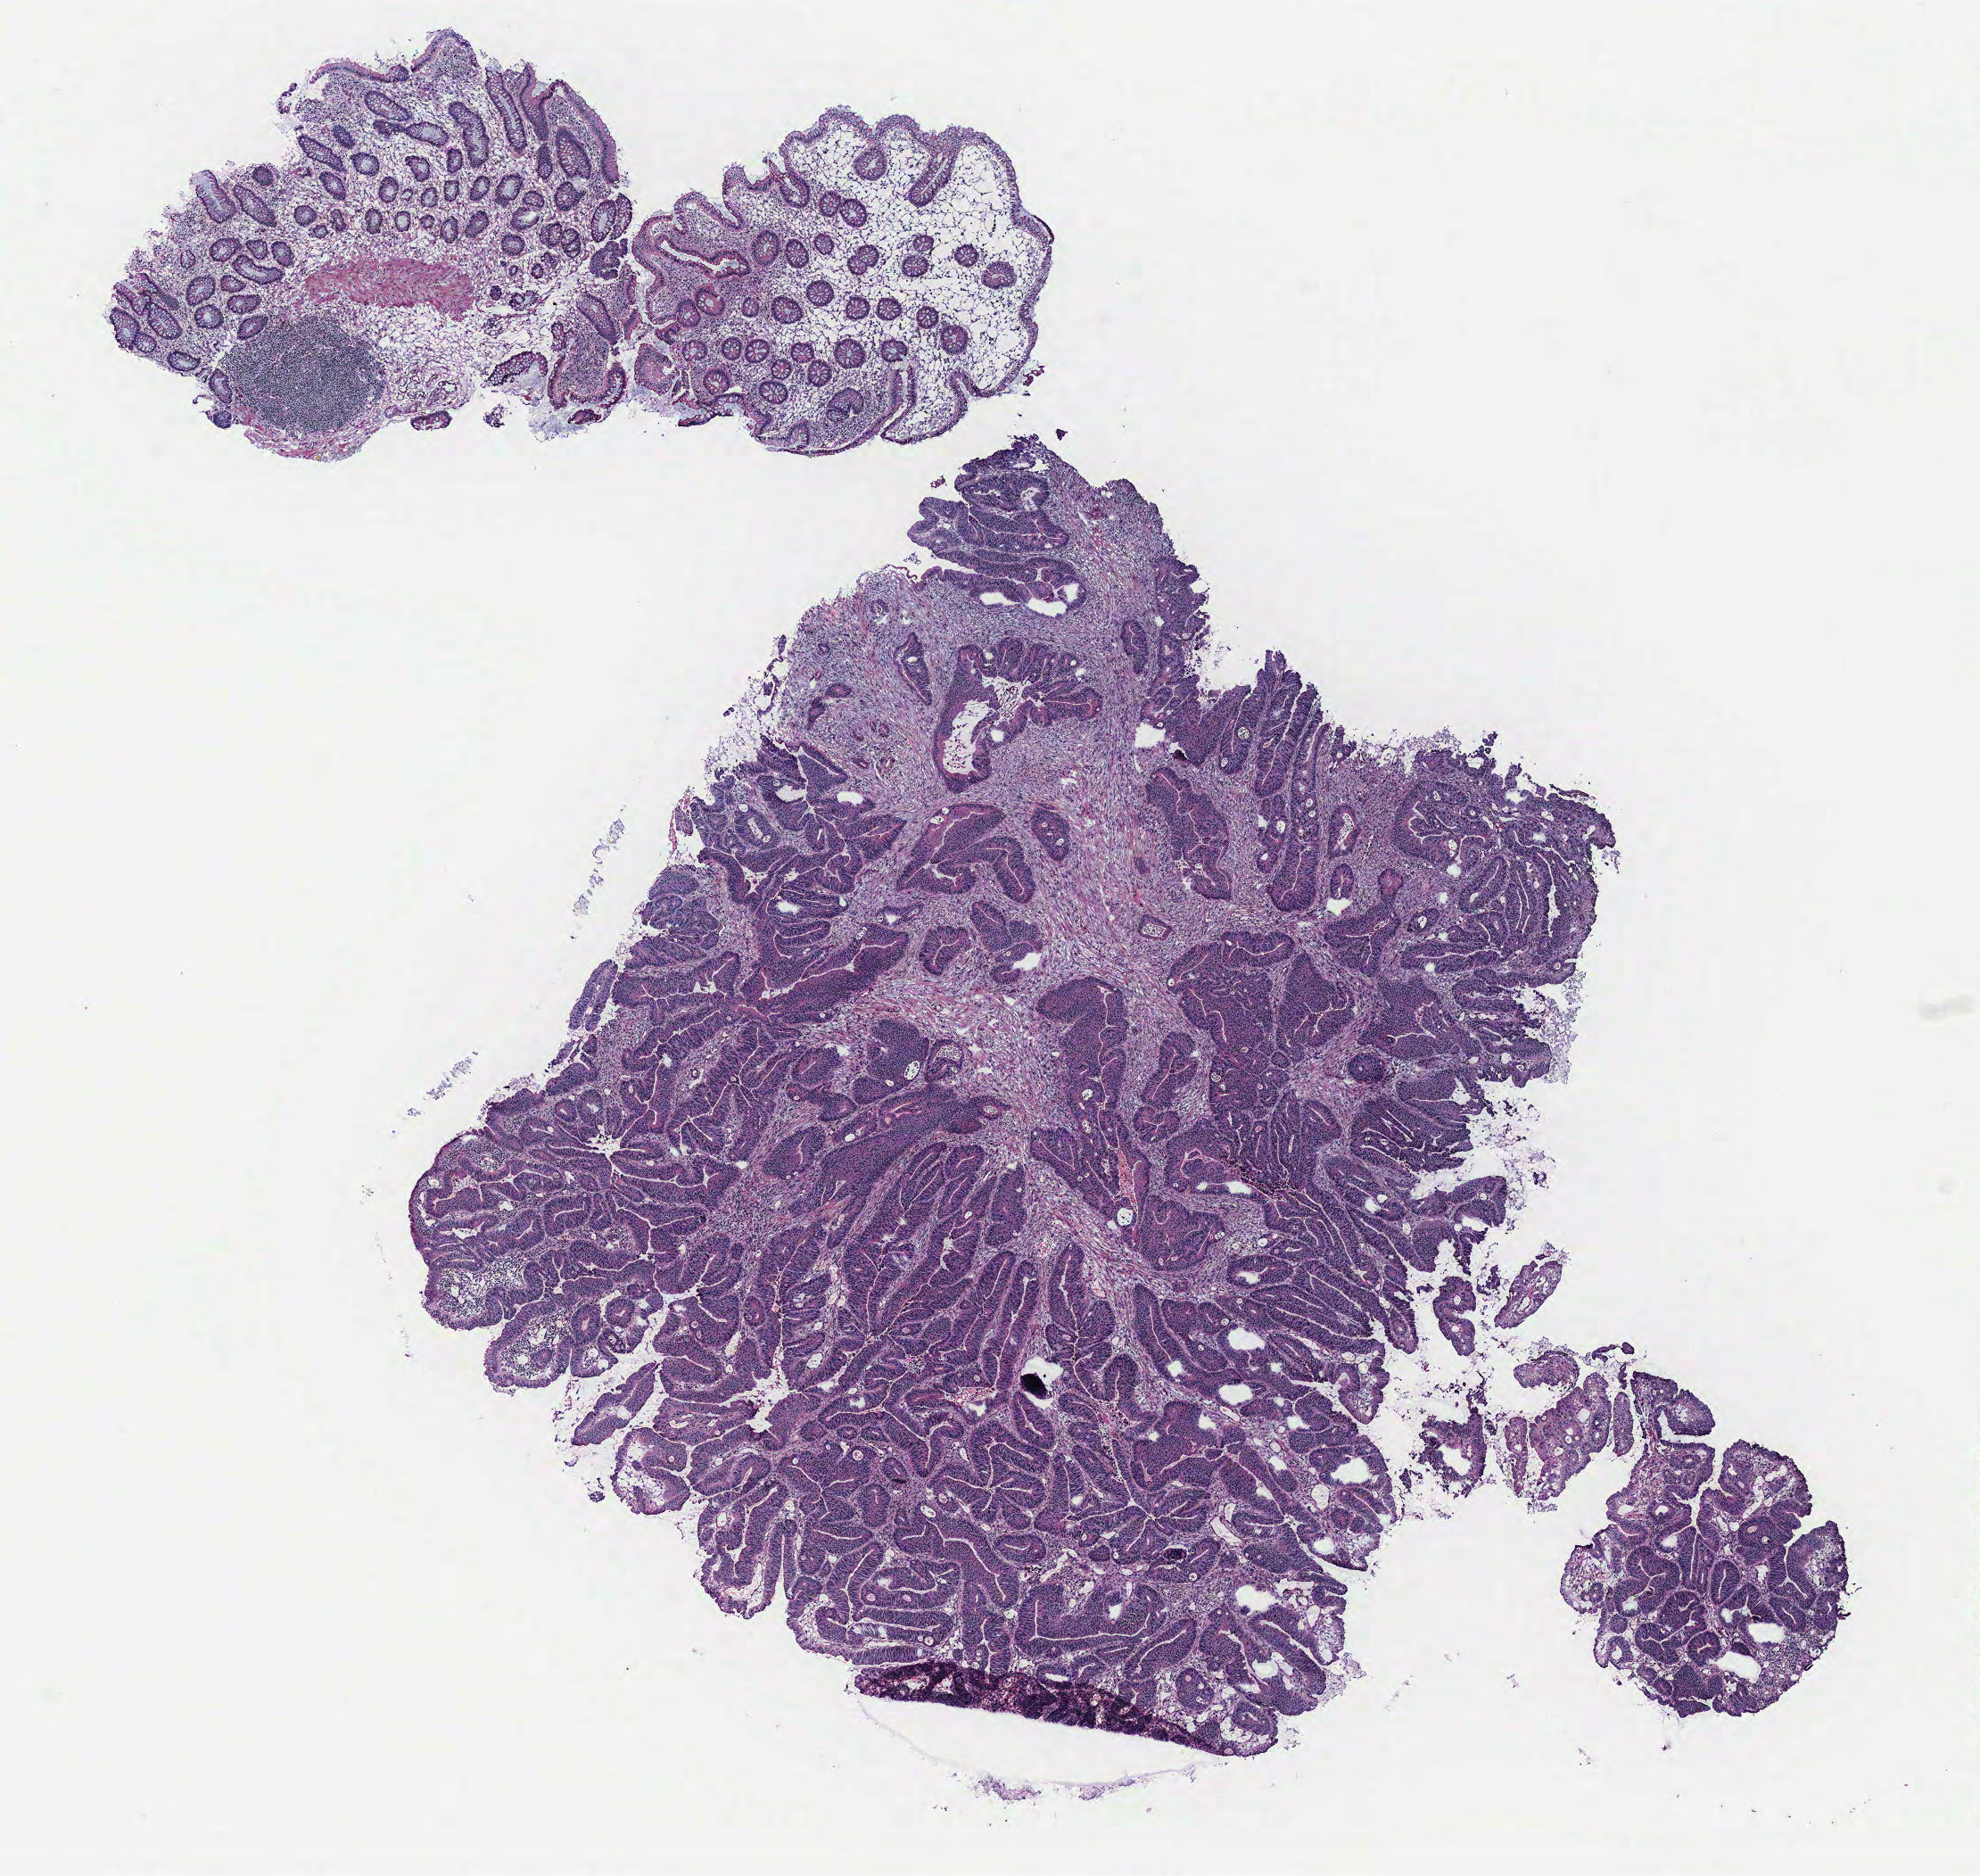
Digitized H&E tissue section (whole slide), a low-resolution overview of the entire scanned area, about 8.9 x 8.4 mm (acquisition: 40x scan), colon, tumour tissue. 86-year-old male patient.
* AJCC pathologic stage: I
* diagnosis: Adenocarcinoma, NOS
* primary tumour site (as recorded): colon